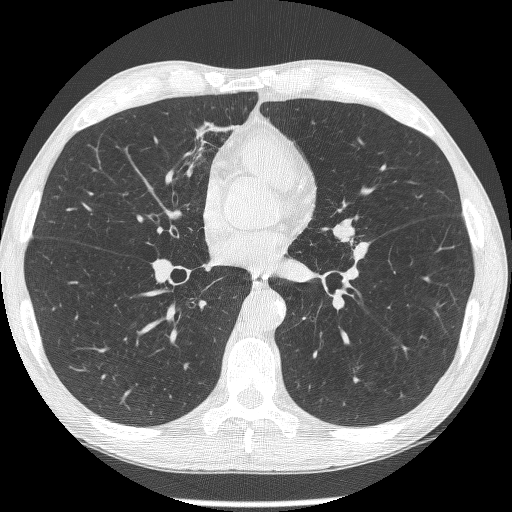
Low-dose screening chest CT, axial slice. Second screening round (one year after baseline). Lung window (W 1500 / L -600 HU). 1.25 mm slice thickness. Lung (sharp) reconstruction kernel (BONE). 512 × 512 image matrix, field of view 326 × 326 mm. Male, age 62 years at enrolment. Former smoker at enrolment.
Expert-annotated lung lesion, bounding box (x1, y1, x2, y2) in pixels: (321, 216, 369, 264). The screening reader recorded 2 non-calcified nodules or masses ≥4 mm on this exam (lingula, lingula); which of them this box marks is not recorded. Participant outcome: lung cancer diagnosed 95 days after this screen — small cell carcinoma, NOS, left upper lobe, stage IIIA (AJCC 6th edition).